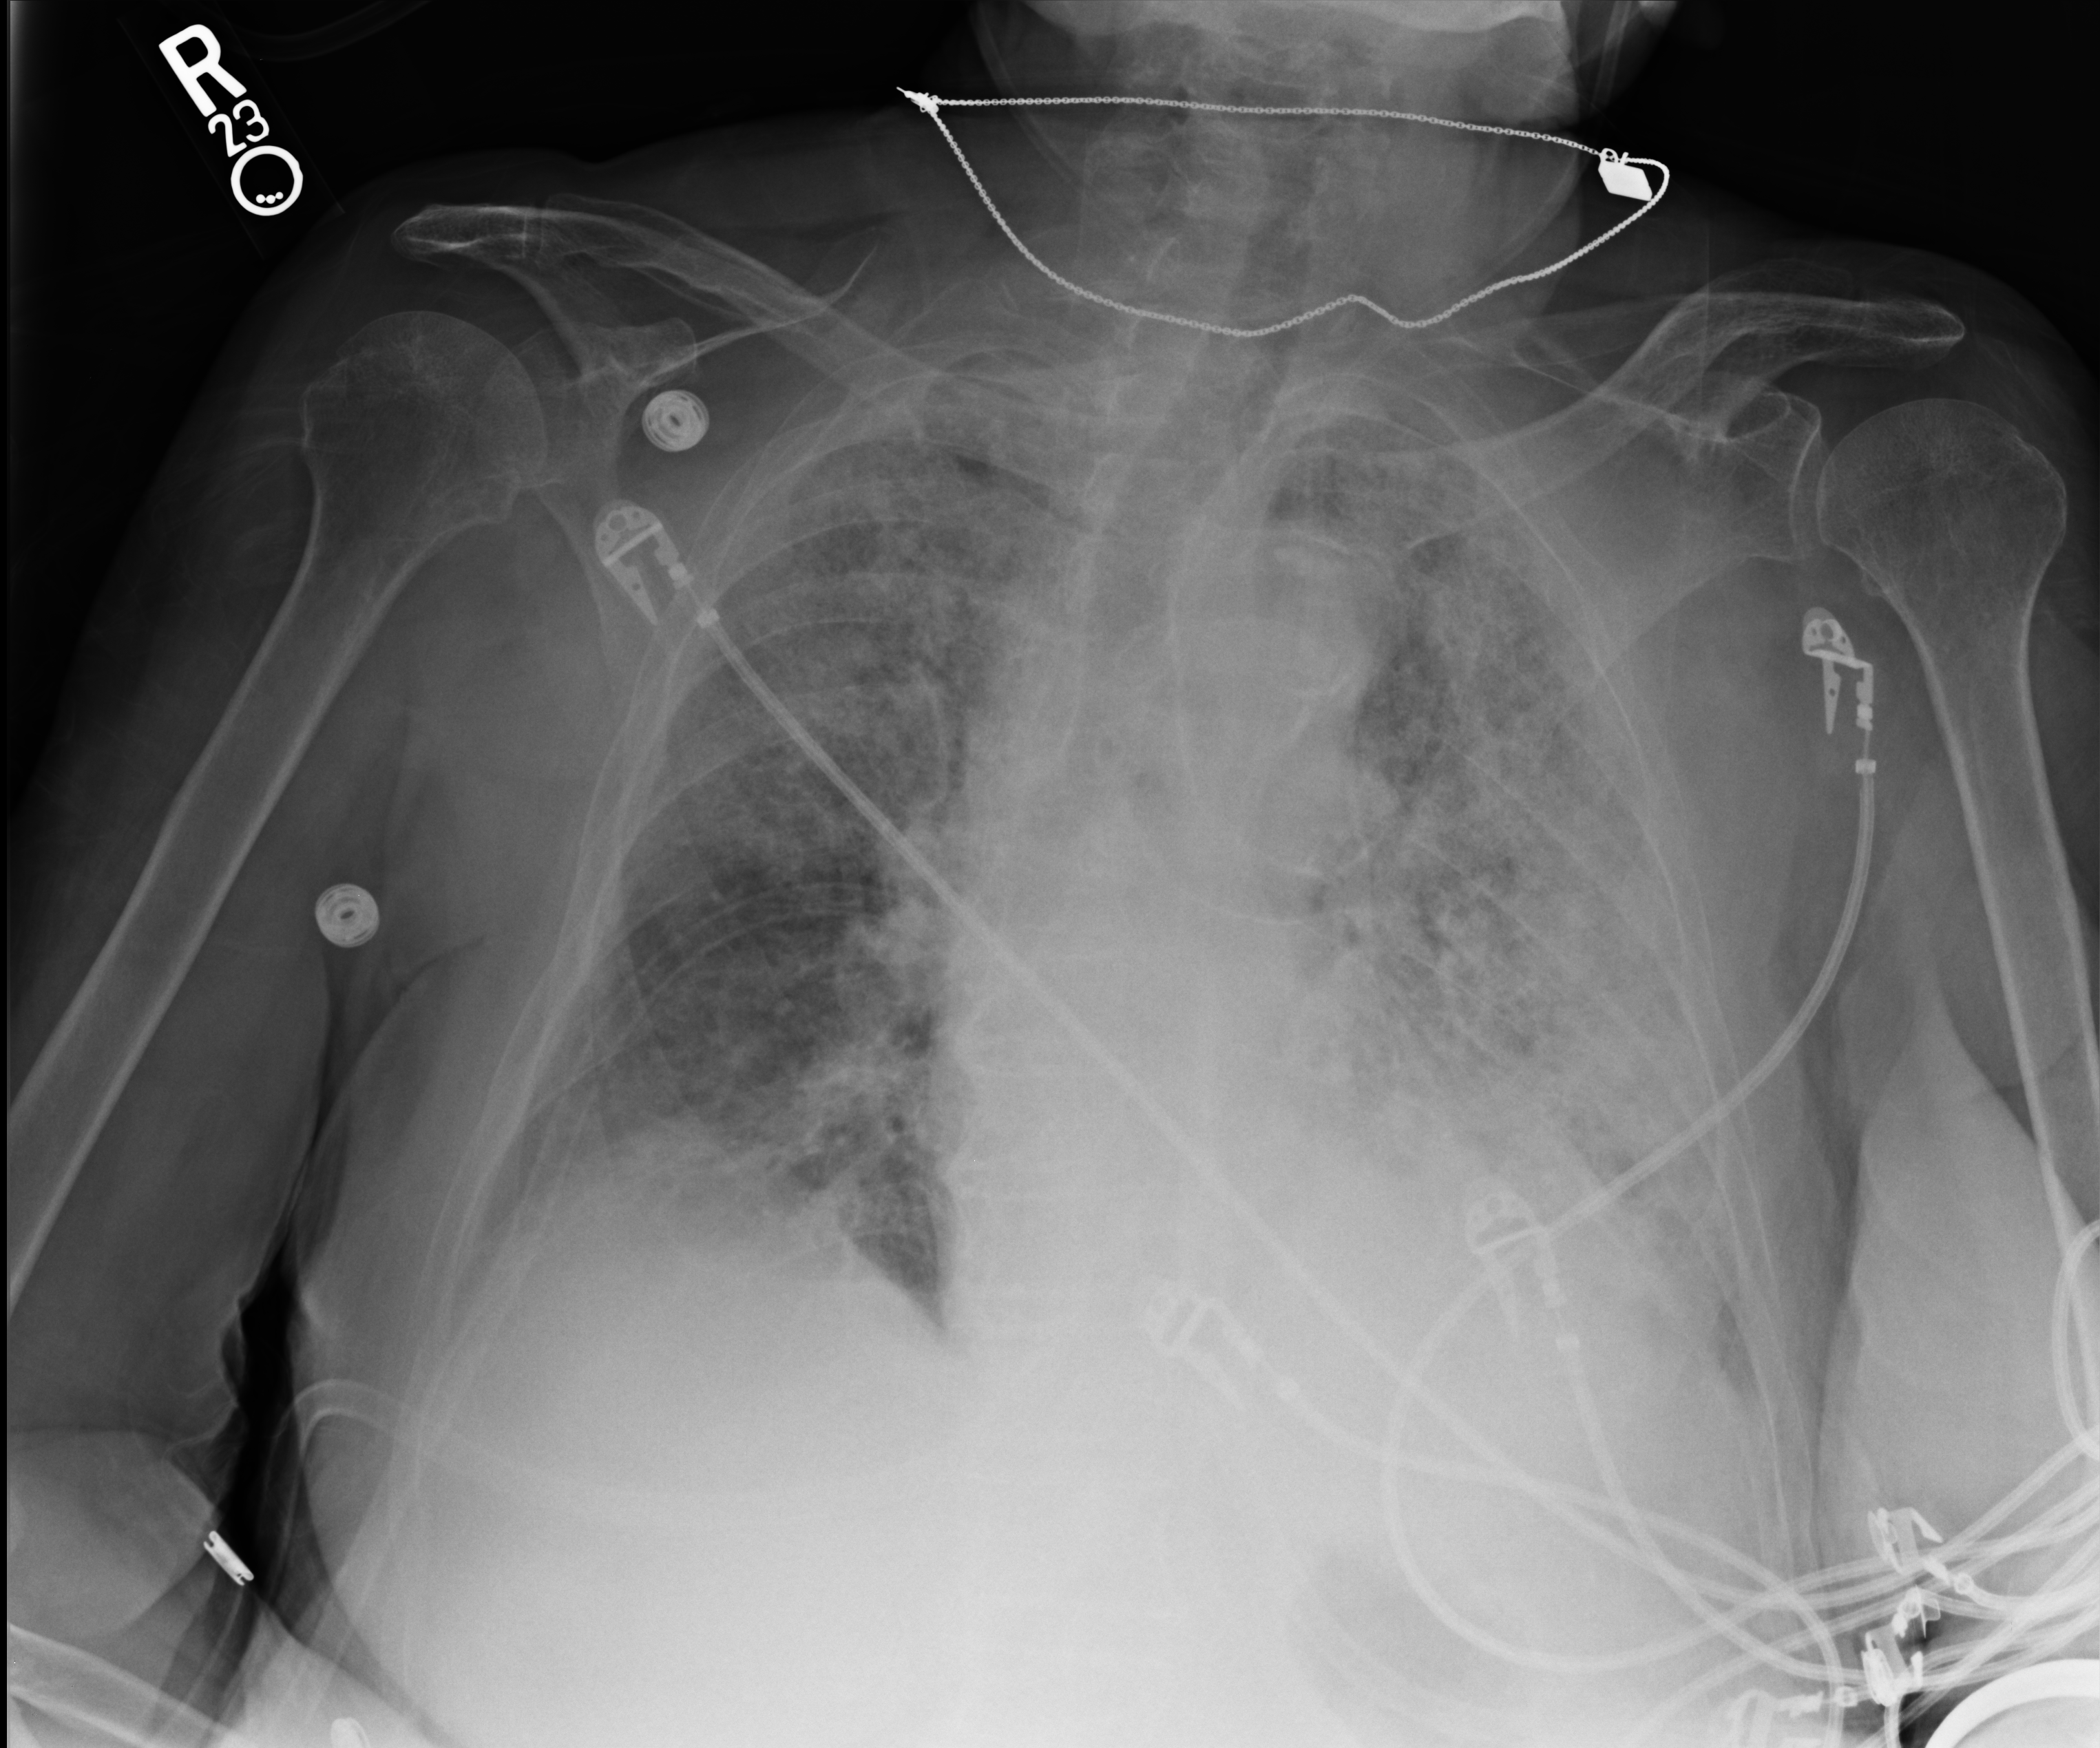
Chest X-ray (portable); anteroposterior (AP) projection. Female patient hospitalised with COVID-19, age 75–90 years.
Hospital-stay facts (about this admission, not read from this image; timing relative to this image not recorded): COPD (admission record): no; mechanically ventilated during this hospital stay: no.